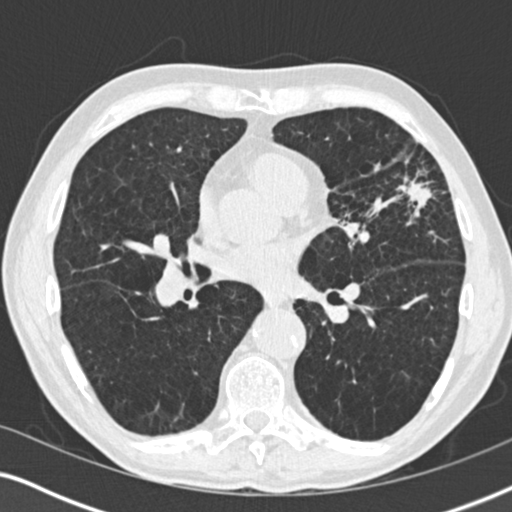
Low-dose screening chest CT, one axial slice; reconstruction kernel B30f; 120 kVp; lung window (W 1500 / L -600 HU); 2 mm slice thickness; 512 × 512 image matrix, field of view 330 × 330 mm.
Annotated regions visible in this slice (outlined manually by an expert reader):
- lesion 1 (tumor, upper lobe of left lung): box from (x=399, y=180) to (x=433, y=205) px